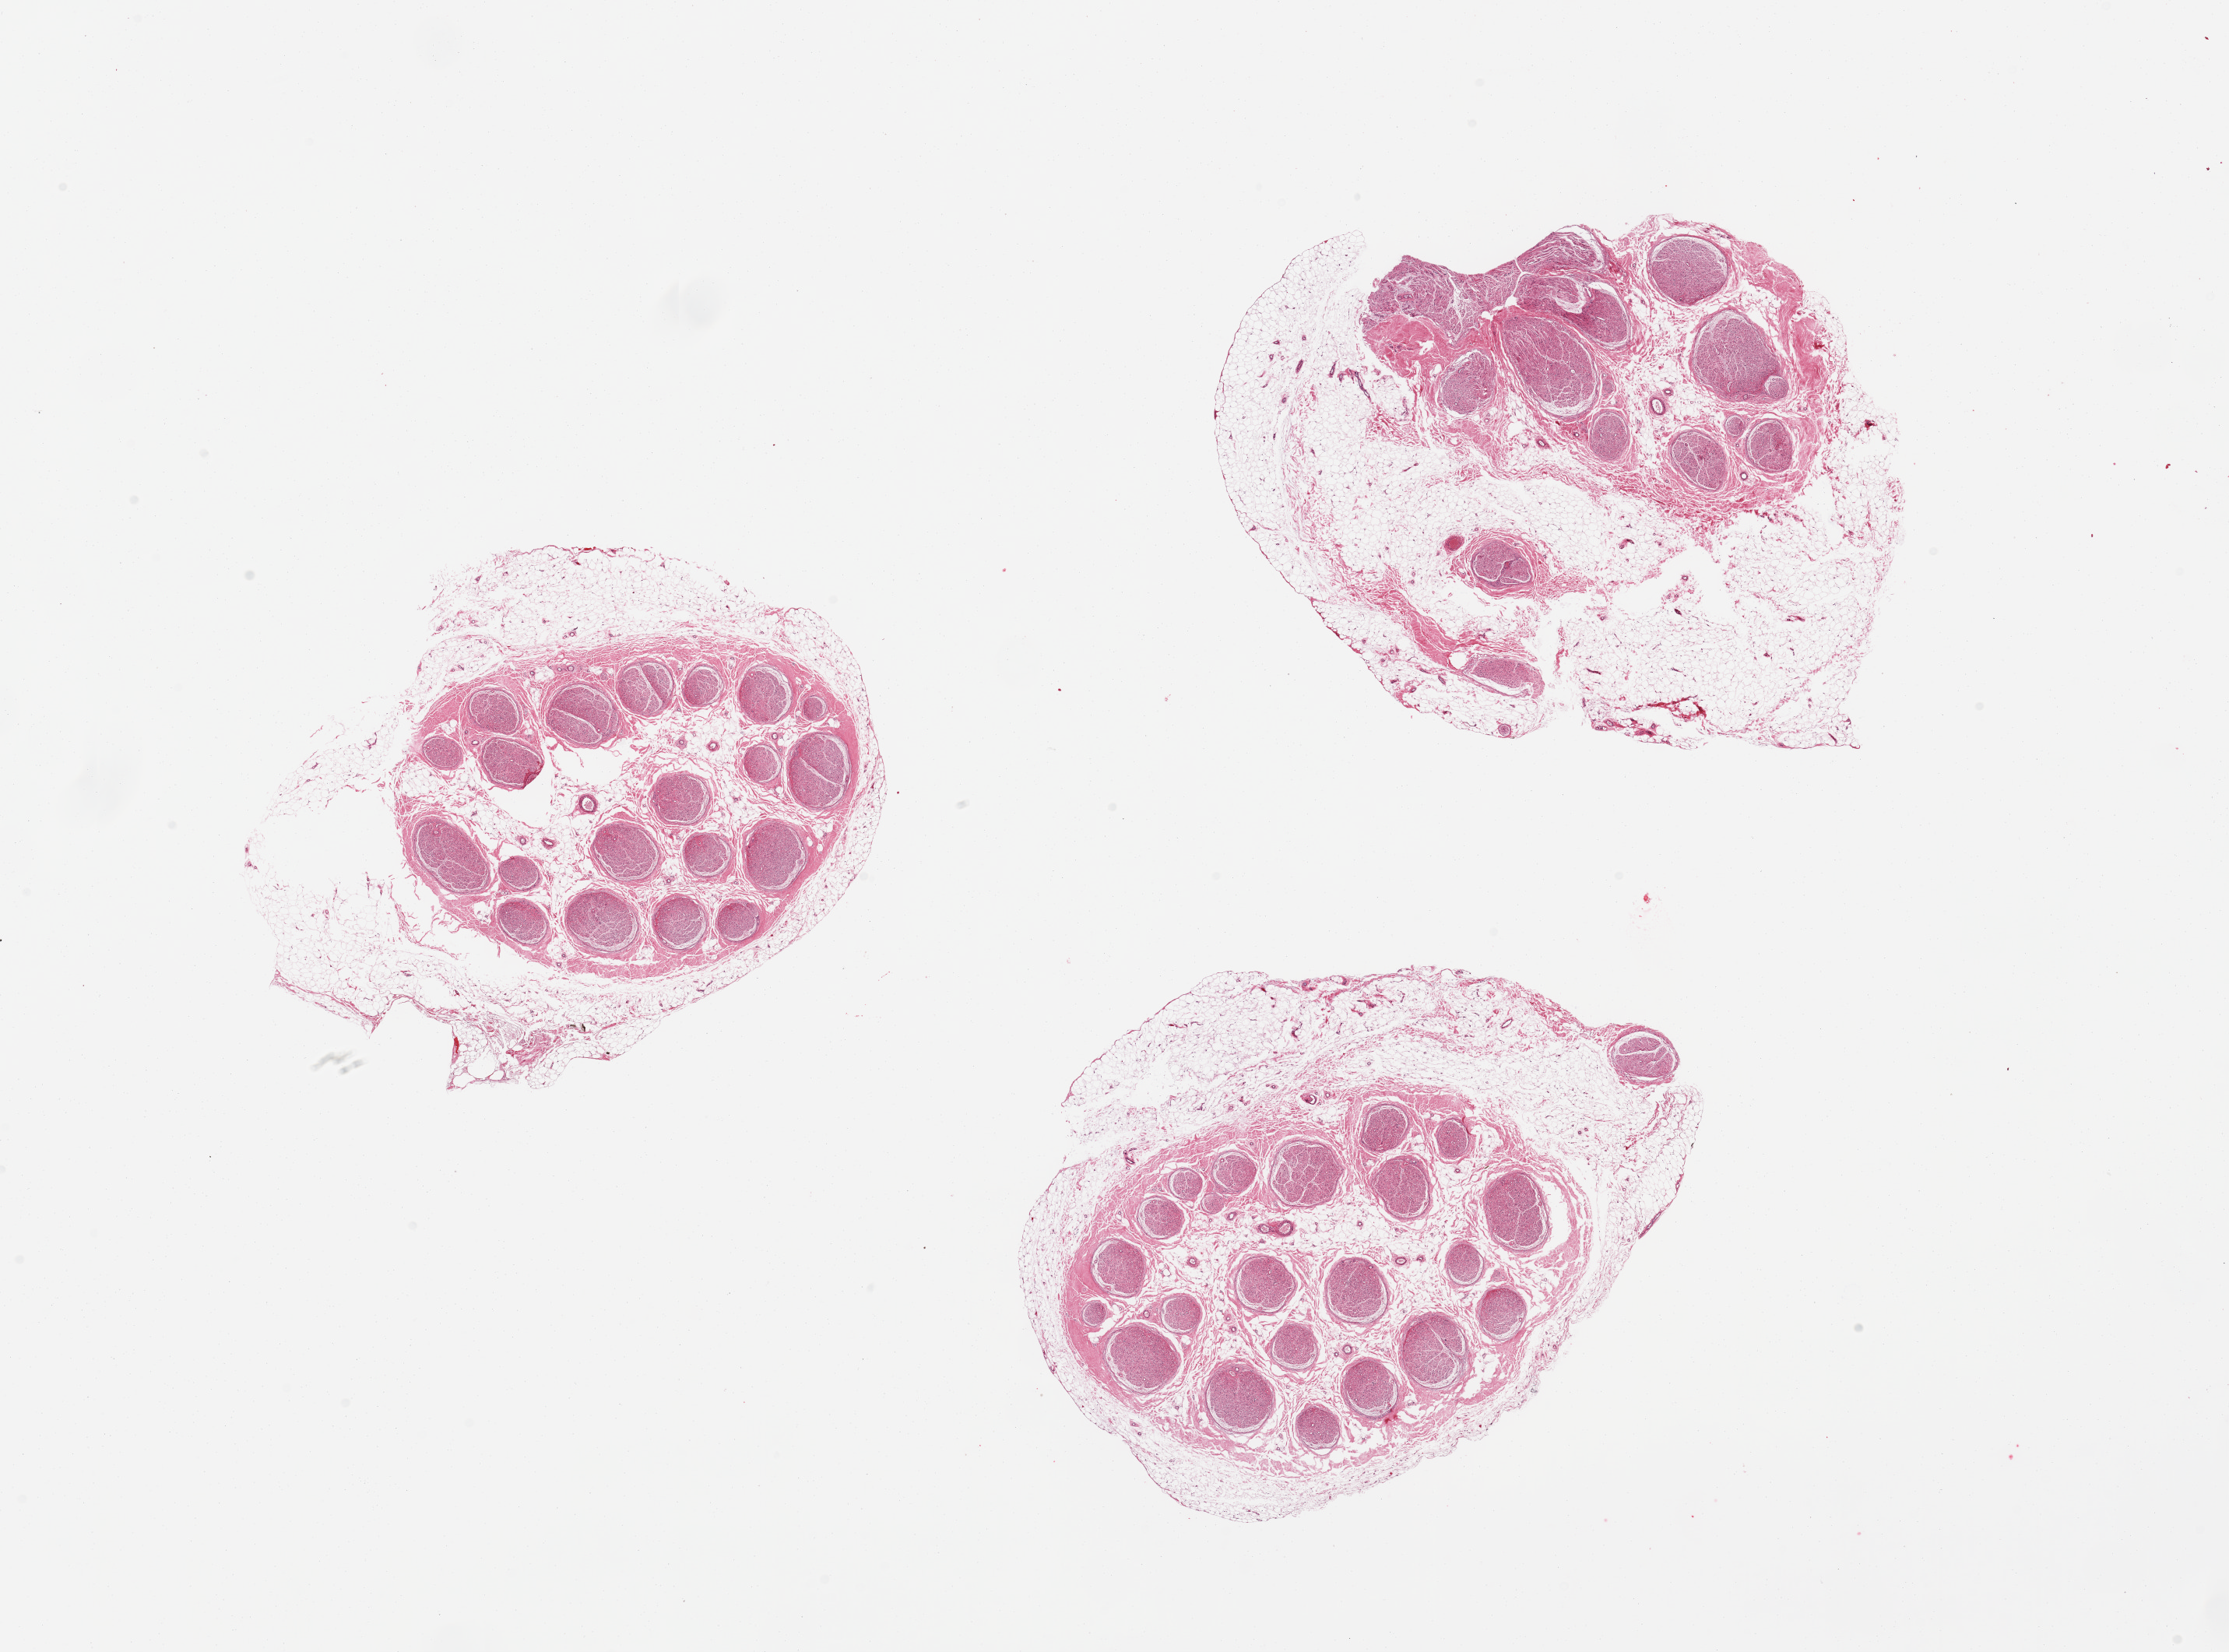
Digitized H&E-stained section, shown as a low-resolution overview of the whole scanned area (about 22.6 x 16.8 mm). PAXgene-fixed paraffin-embedded (PFPE) section. Section of tibial nerve (target tissue). Tissue donor sample. Donor sex: male.
* review note (as recorded): 3 pieces, adherent rims of fat up to ~2.5mm